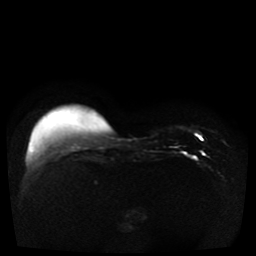
Breast MRI, one axial slice. Position 7 of 41 along the scan axis. Diffusion-weighted series; image 2 of 4 stored at this slice position (different b-values; order by instance number). 1.5 T. 256 × 256 image matrix, field of view 330 × 330 mm. Female patient.
Annotated regions visible in this slice (expert manual segmentation):
- tumour on diffusion-weighted imaging: bounding box <196,135,203,140> (left, top, right, bottom; pixels)